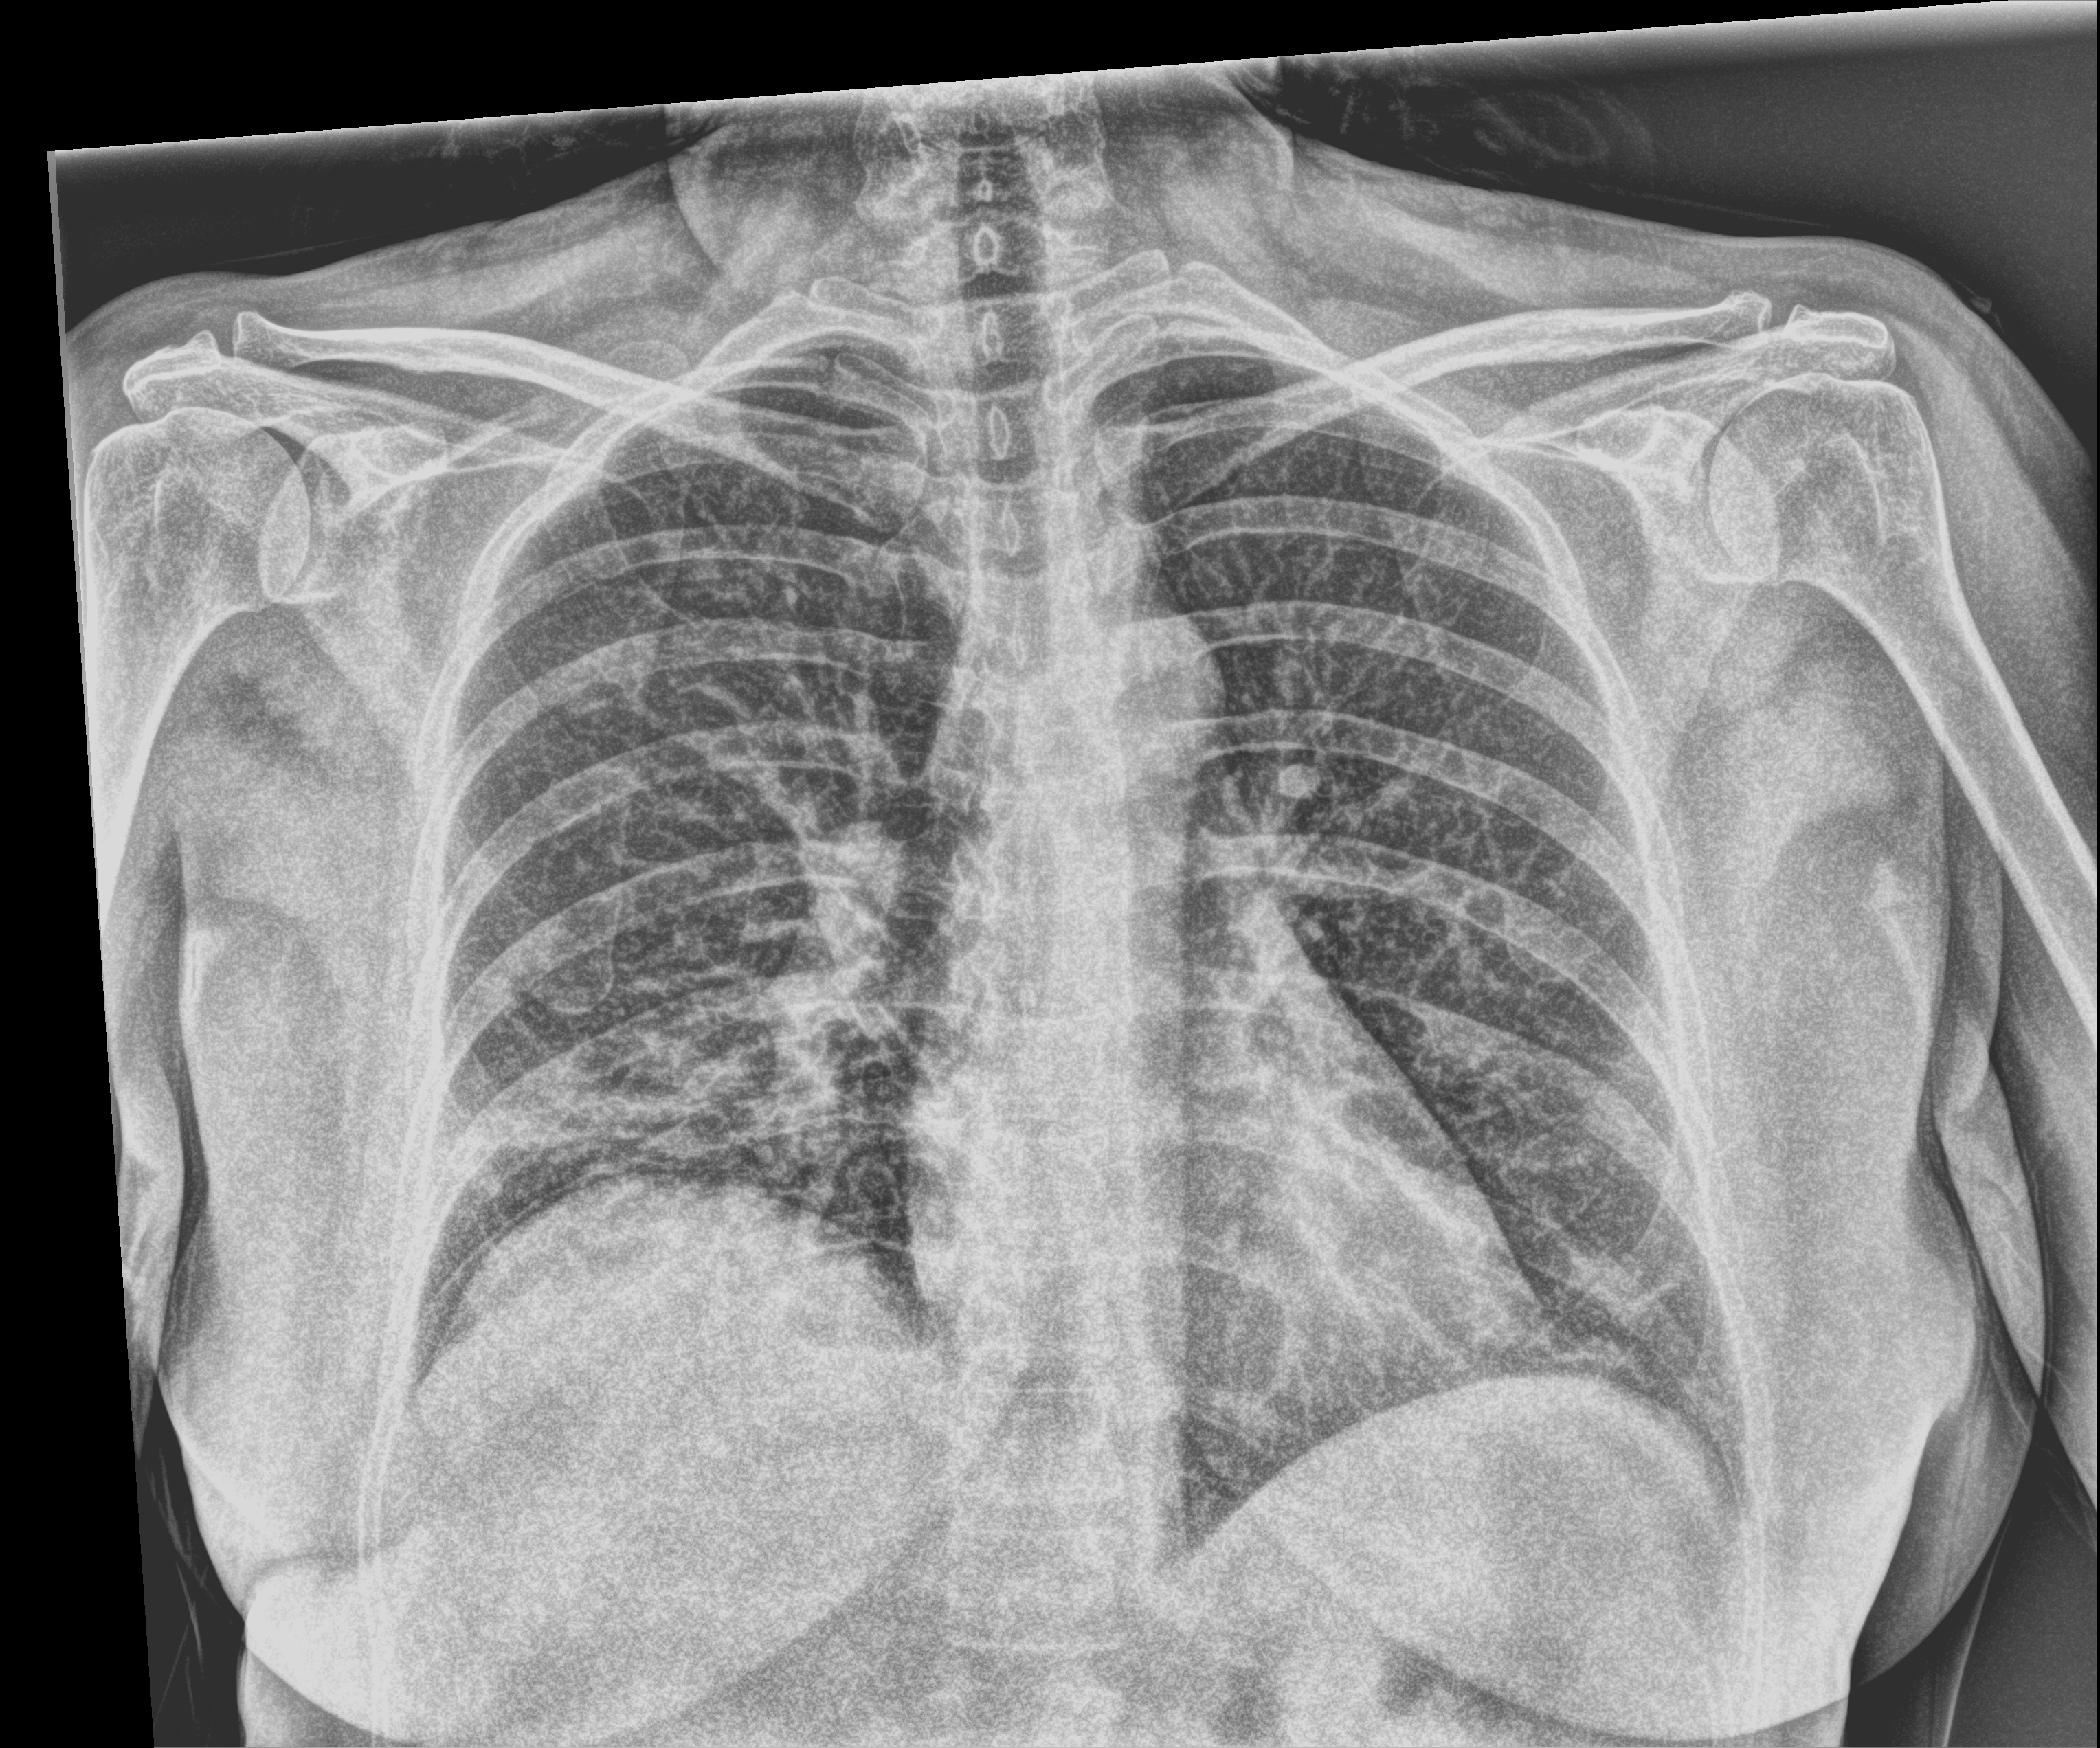
Portable chest radiograph, anteroposterior (AP) projection. Female patient hospitalised with COVID-19, age 18–59 years.
From the hospital-stay record, not from the radiograph (when in the stay this image was taken is not recorded): admitted to intensive care during this hospital stay: no; mechanically ventilated during this hospital stay: no; length of hospital stay: 1 day.